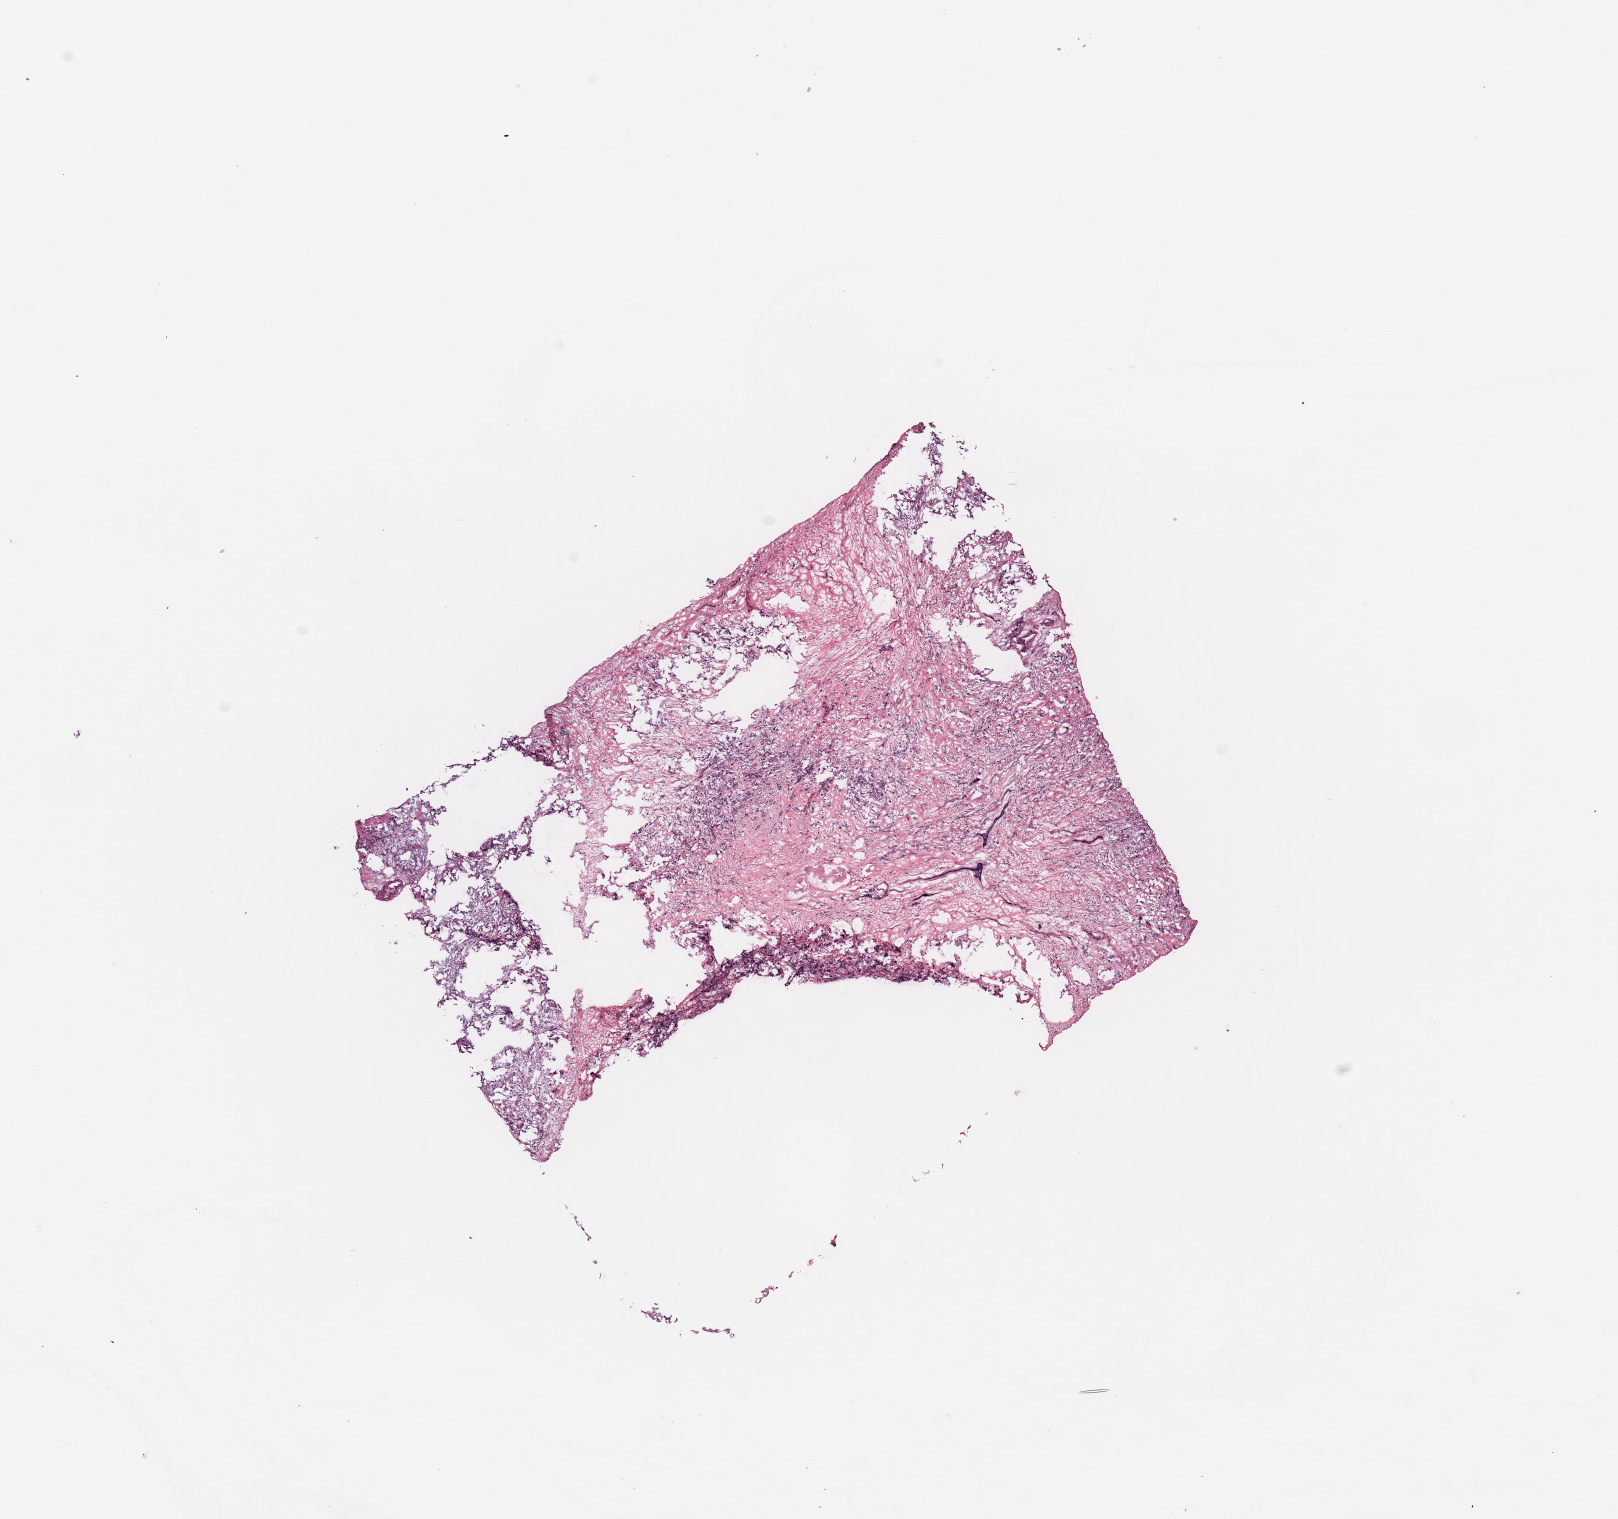
Whole-slide histology image, H&E — low-resolution overview of the scanned area, about 12.8 x 12.0 mm (slide scanned at 20x), tumour tissue sample, breast. Patient: female, age 71 years.
Histologic diagnosis: Infiltrating lobular carcinoma, NOS. AJCC pathologic stage: IIA.